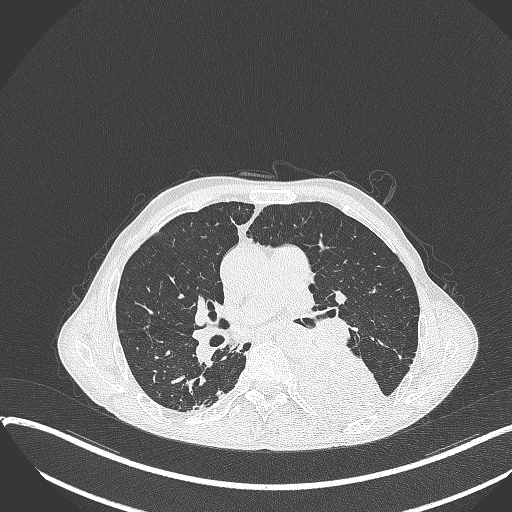
Chest CT, one axial slice; position 212 of 401 along the scan axis; reconstruction kernel B70f; 120 kVp; lung window (W 1500 / L -600 HU); 1 mm slice thickness; 512 × 512 image matrix. Patient: male, 57 years. Case-level facts recorded for this patient, not image findings: clinical TNM (as recorded): T4 N0 M0.
Outlined on this slice (rectangle marked by the reading radiologist):
- lung tumour (recorded histology: squamous cell carcinoma): bounding box (x1, y1, x2, y2) in pixels: (289, 349, 389, 428)